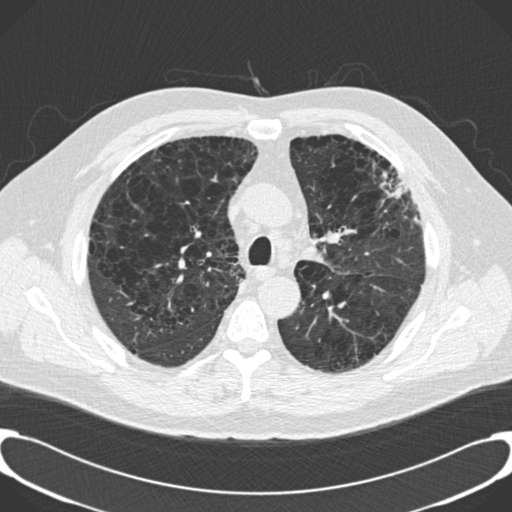
Low-dose screening chest CT, one axial slice. Slice 140 of 189 in the series (ordered by position). 120 kVp. Lung window (W 1500 / L -600 HU). 2 mm slice thickness. 512 × 512 image matrix.
Annotated regions visible in this slice (manually delineated by an expert):
- lesion 1 (tumor, upper lobe of left lung): box from (x=392, y=180) to (x=408, y=198) px